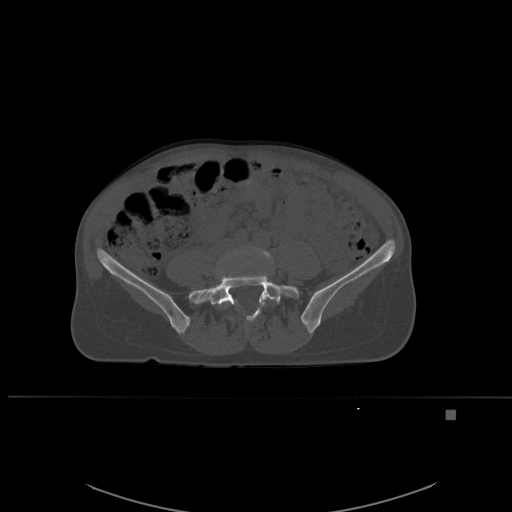
CT including the spine, one axial slice; position 178 of 537 along the scan axis; bone window (W 1800 / L 400 HU); 512 × 512 image matrix, field of view 440 × 440 mm. Female patient, age 45 years. From the clinical record (not read from this slice): primary cancer: lung.
Structures marked on this image (semi-automatic segmentation, software-assisted and operator-edited):
- L4 vertebra: bounding box <220,246,273,308> (left, top, right, bottom; pixels)
- L5 vertebra: <196,272,299,321>